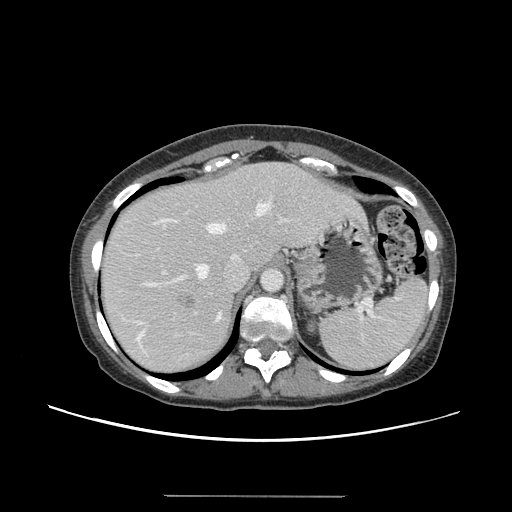
Contrast-enhanced abdominal CT, one axial slice. Slice 111 of 144 in the series (ordered by position). 120 kVp. Intravenous contrast given. Soft-tissue window (W 400 / L 40 HU). 2.5 mm slice thickness. 512 × 512 image matrix. Female patient, age 53 years. From the clinical record (not read from this slice): diagnosis: colorectal cancer liver metastases, imaged before liver resection; multiple liver metastases: yes; largest metastasis: 1.1 cm; chemotherapy before resection: no.
Structures marked on this image (manually delineated by an expert):
- hepatic veins: bounding box <137,203,269,339> (left, top, right, bottom; pixels)
- liver: <101,163,363,372>
- planned liver remnant (the part of the liver to remain after resection): <100,163,294,301>
- portal vein (with intrahepatic branches): <153,219,288,274>
- liver metastasis: <178,295,195,308>
- liver metastasis: <167,357,170,360>